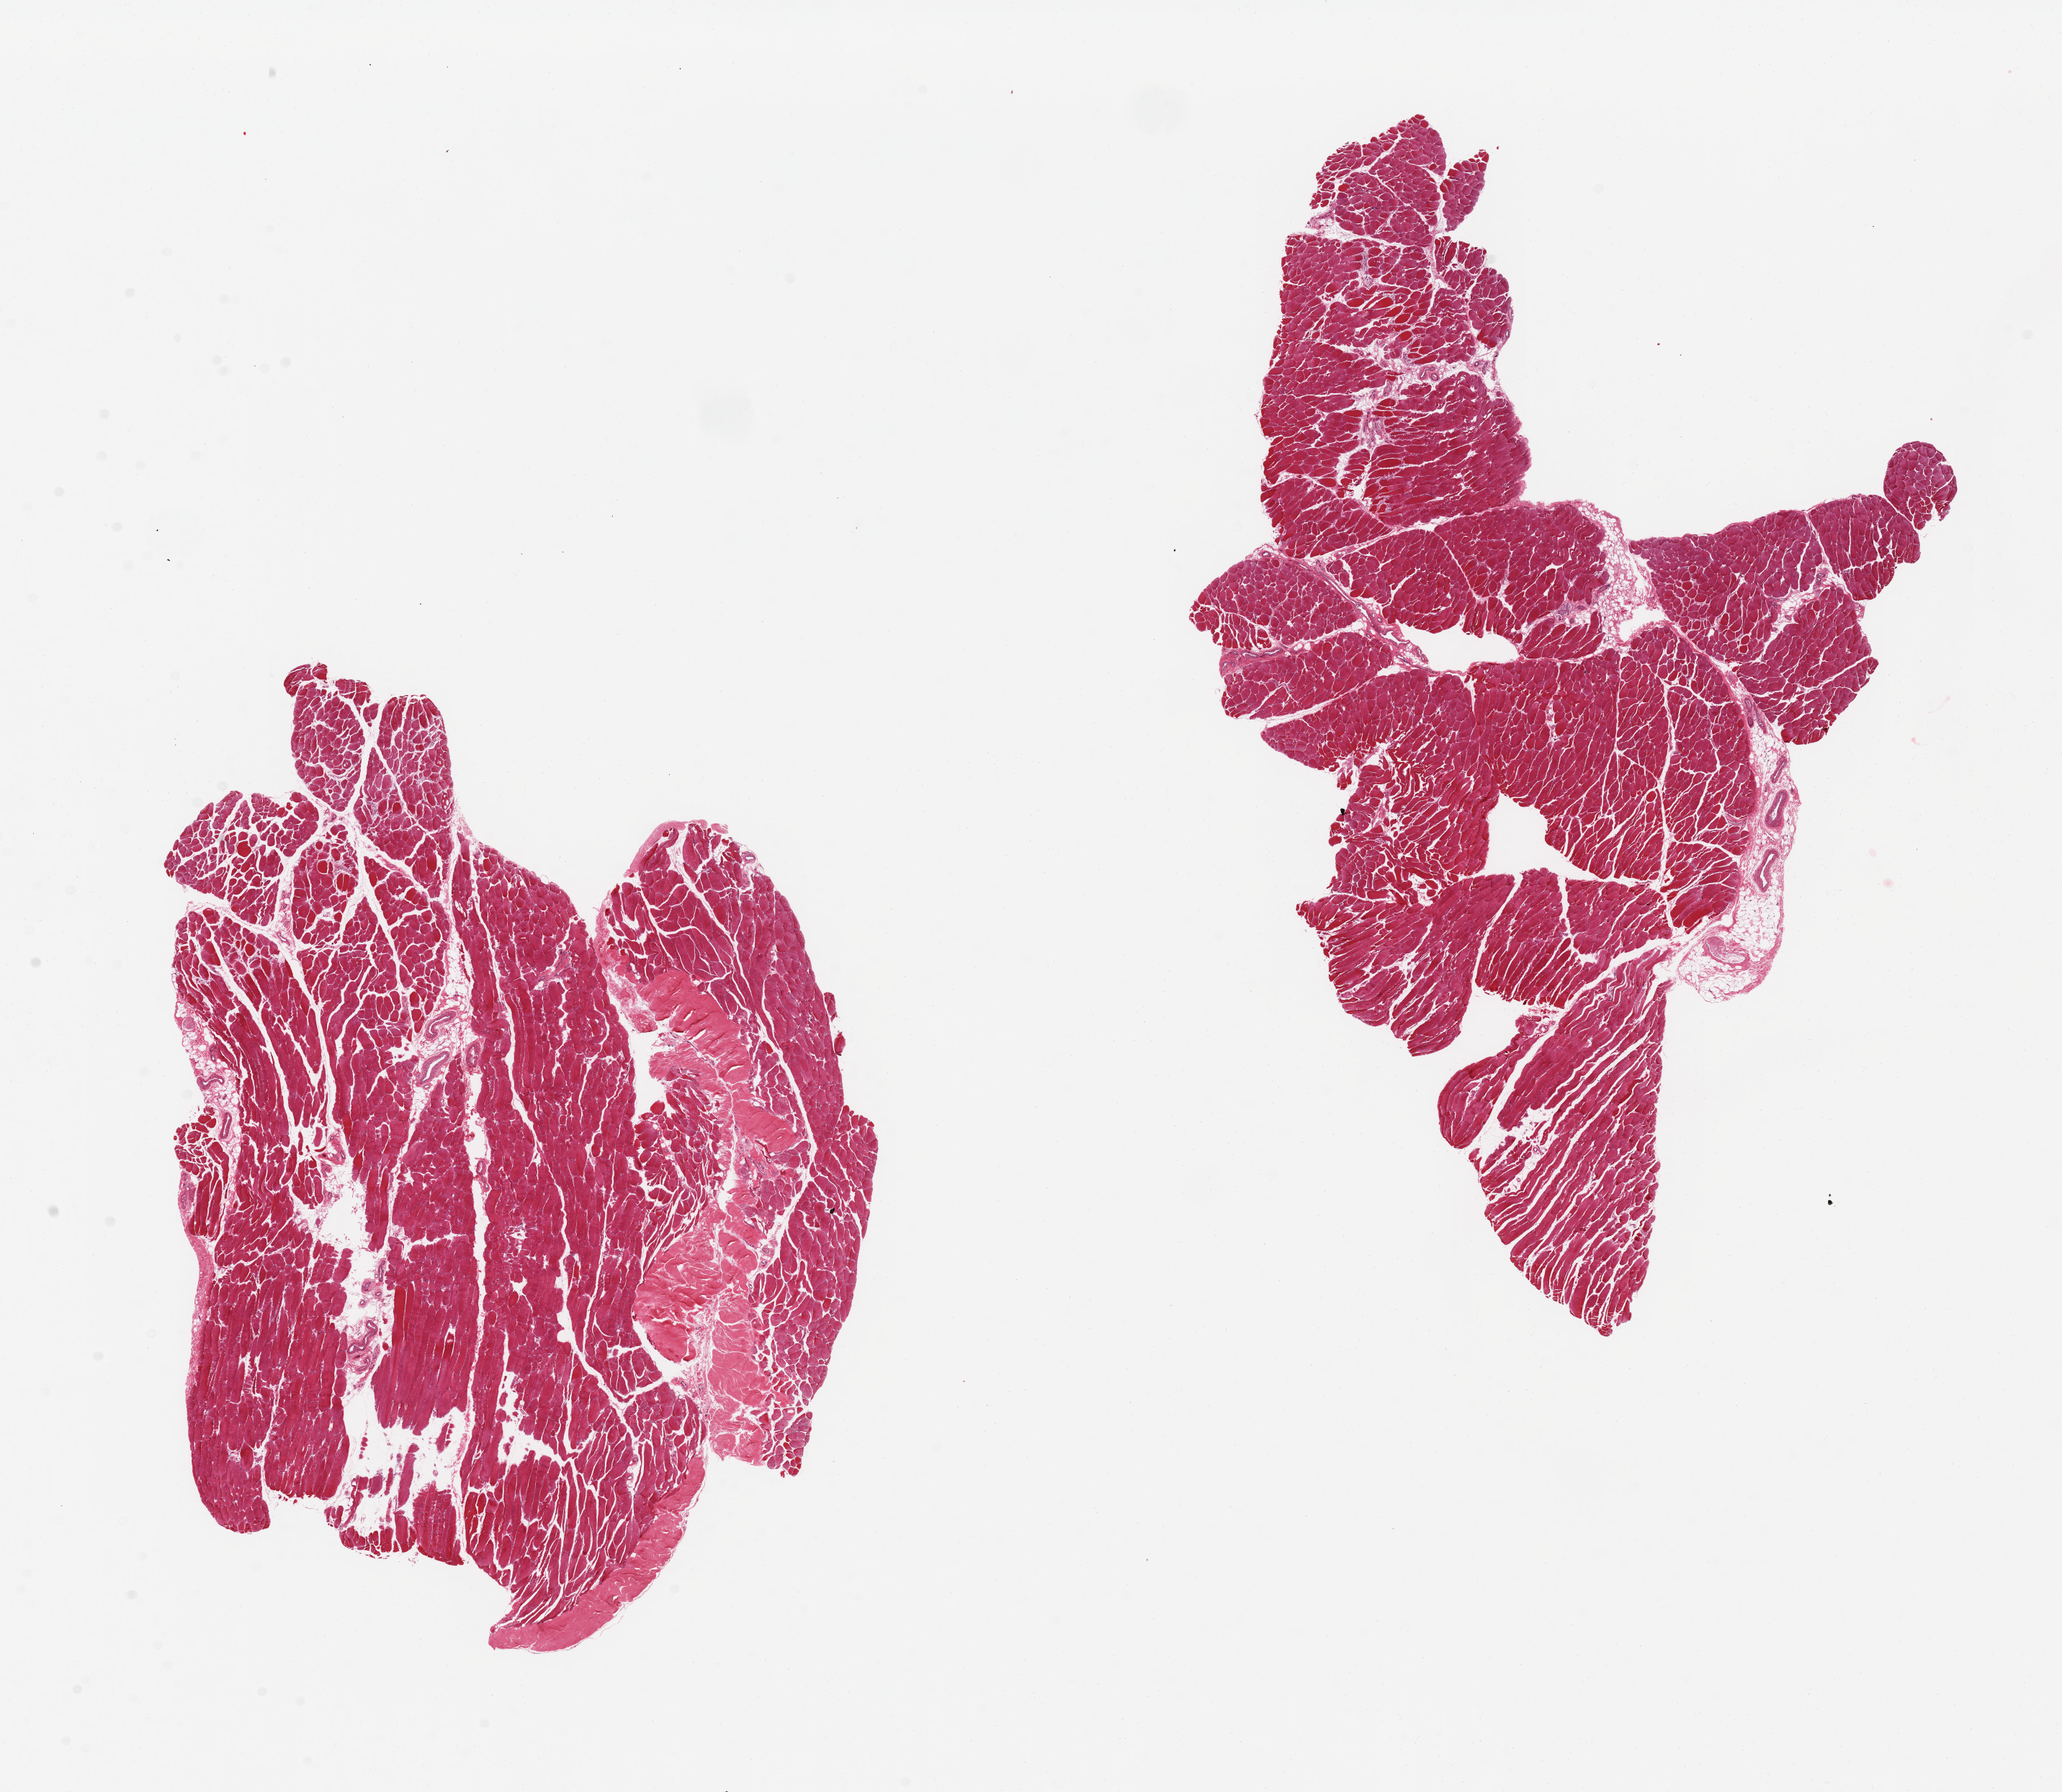
Digitized hematoxylin and eosin (H&E)-stained section — low-resolution overview of the scanned area, about 22.6 x 19.7 mm (acquisition: 20x scan), PAXgene-fixed paraffin-embedded (PFPE) section, target tissue: skeletal muscle, tissue donor sample. Donor sex: male.
Pathologist's review note for this sample: 2 pieces.